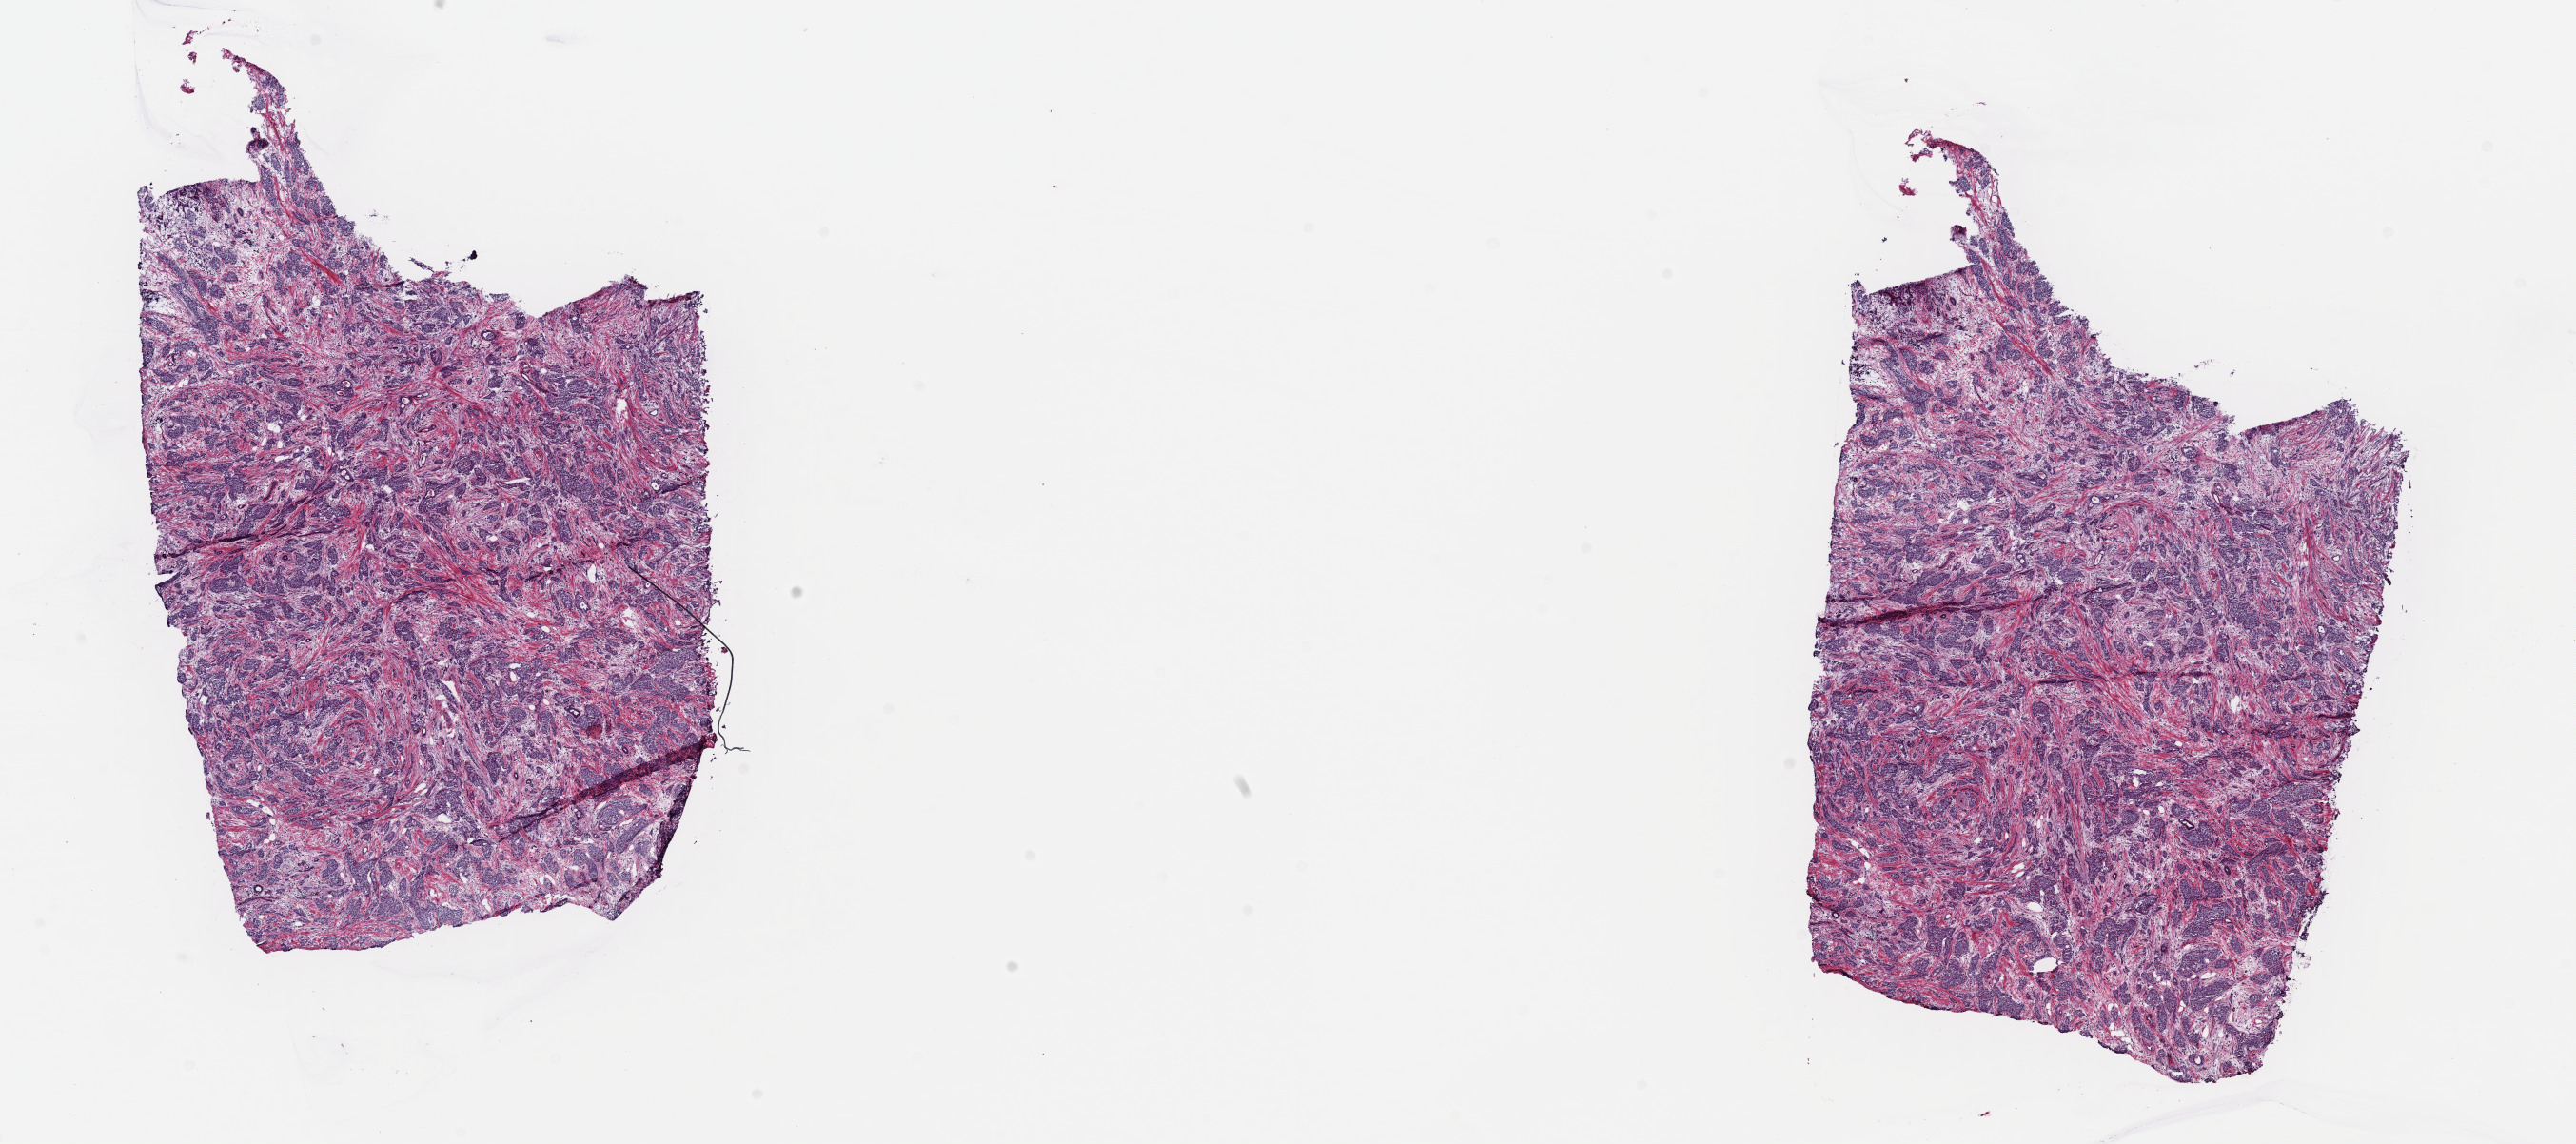
Digitized H&E-stained tissue section (whole slide), whole scanned area (about 21.4 x 9.5 mm) shown as a low-resolution overview. Frozen section from the top of the tissue portion. Sample: primary tumour, breast. Female patient; age at initial diagnosis 56 years. Composition of this section per pathologist review: tumour cells 70%, tumour nuclei 80%, normal cells 0%, stromal cells 30%, necrosis 0%. Inflammatory infiltration, as recorded: lymphocyte infiltration 0%, monocyte infiltration 0%, neutrophil infiltration 0%.
Lymph nodes positive (case pathology): 0 of 1 examined. Pathologic diagnosis: Infiltrating duct carcinoma, NOS. AJCC pathologic stage: IA (7th edition).